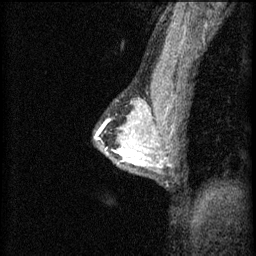
Breast MRI (dynamic contrast-enhanced), one sagittal slice. Slice 42 of 60 in the series (ordered by position). 3 images stored at this slice position (order not interpretable as contrast timing). 1.5 T. TE 4.2 ms, TR 8.2 ms. 2 mm slice thickness. 256 × 256 image matrix, field of view 180 × 180 mm. Patient: female, 44 years.
Structures marked on this image (semi-automatic segmentation, software-assisted and operator-edited):
- analysis volume of interest (the breast-tissue region the enhancement analysis was run in; not a lesion): box from (x=102, y=132) to (x=151, y=165) px
- tumour enhancement mask (voxels above the 70 % enhancement threshold inside the analysis volume of interest): (x=120, y=132)–(x=151, y=163)